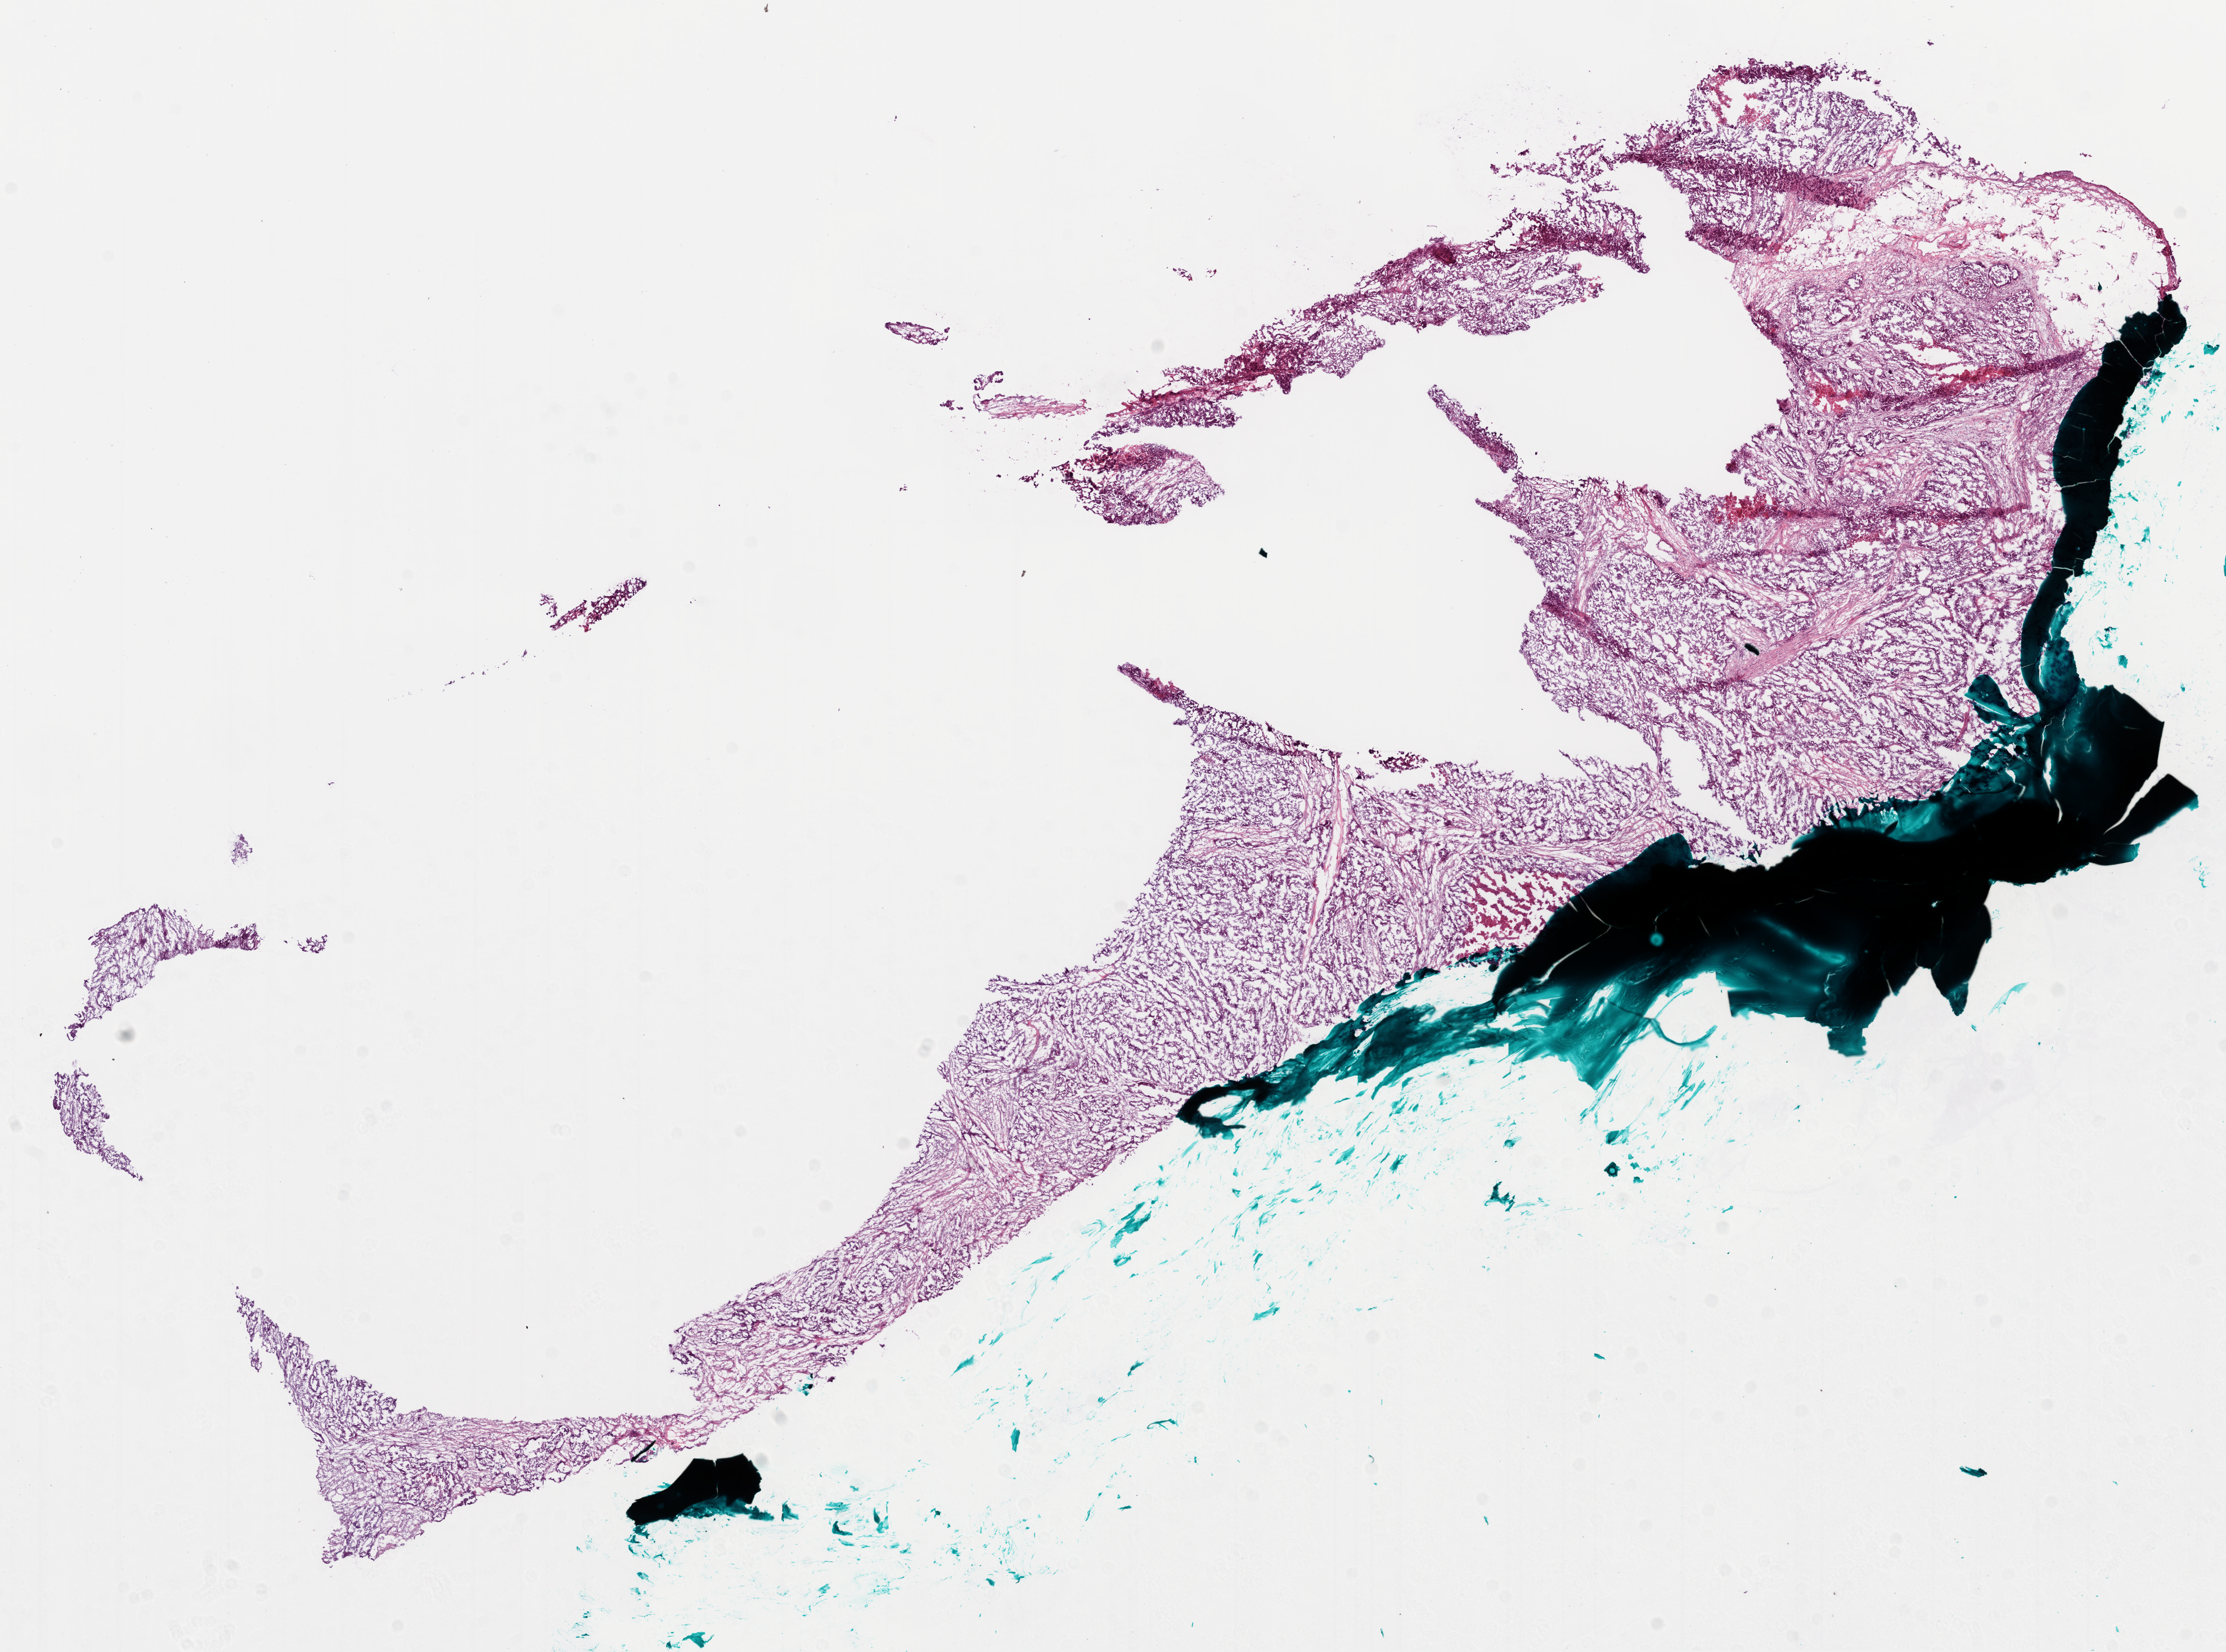
Whole-slide histology image, H&E-stained, low-resolution overview of the scanned area, about 16.0 x 11.8 mm; frozen section; primary tumour sample from the ovary. Patient: female, age at initial diagnosis 42 years. Histologic grade: G3 (poorly differentiated). Slide review estimates, as recorded: tumour cells 79%, tumour nuclei 80%, normal cells 20%, necrosis 1%.
Histologic diagnosis: Serous cystadenocarcinoma, NOS. FIGO stage: IIIC. Laterality: bilateral.